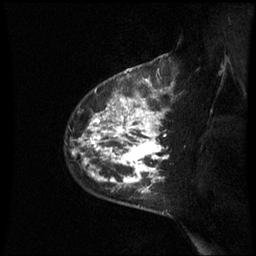
Breast MRI (dynamic contrast-enhanced), one sagittal slice. Position 47 of 60 along the scan axis. Dynamic contrast-enhanced series, image 2 of 3 at this slice position (ordered by acquisition). 1.5 T. TE 4.2 ms, TR 8.9 ms. 2.4 mm slice thickness. 256 × 256 image matrix. Female patient, age 42 years. Case-level facts recorded for this patient, not image findings: setting: breast cancer imaged before/during neoadjuvant chemotherapy; receptor status: HER2-positive.
Outlined on this slice (semi-automatically segmented with operator editing):
- analysis volume of interest (the breast-tissue region the enhancement analysis was run in; not a lesion): bounding box <73,93,171,210> (left, top, right, bottom; pixels)
- tumour enhancement mask (voxels above the 70 % enhancement threshold inside the analysis volume of interest): <82,98,168,194>